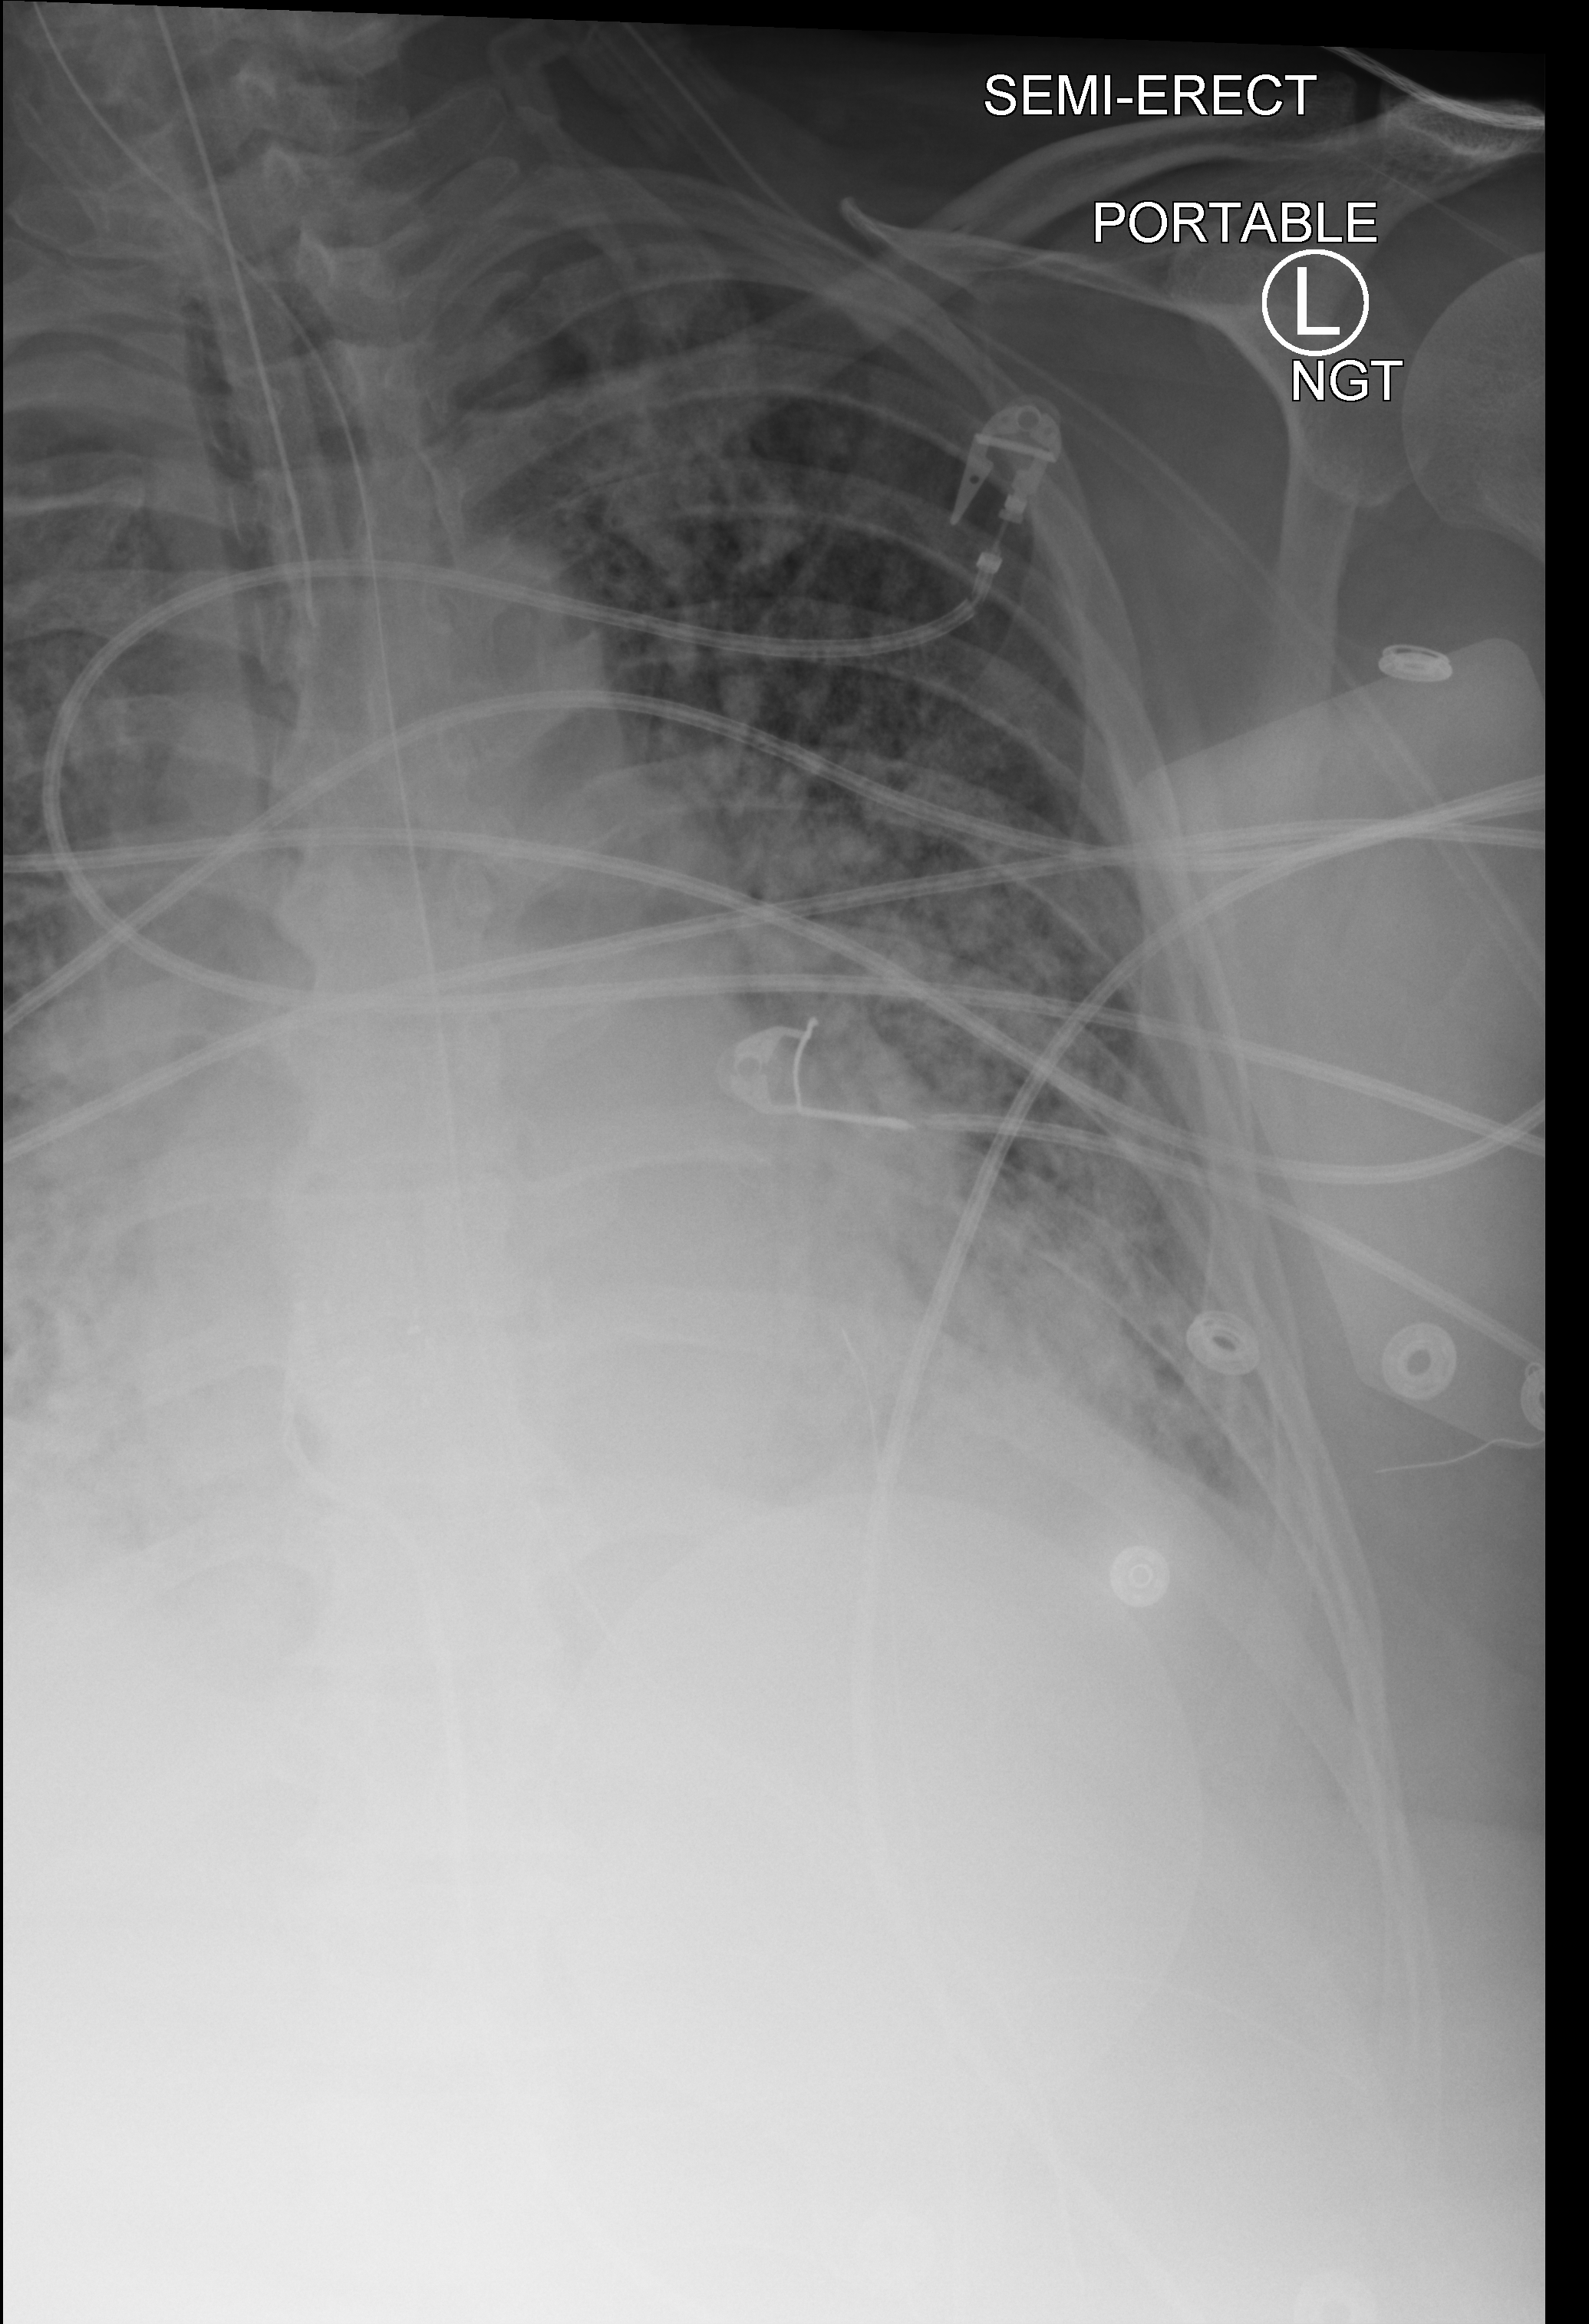
Chest X-ray (portable); anteroposterior (AP) projection. Male patient hospitalised with COVID-19, age 60–74 years.
From the hospital-stay record, not from the radiograph (when in the stay this image was taken is not recorded): mechanically ventilated during this hospital stay: yes.